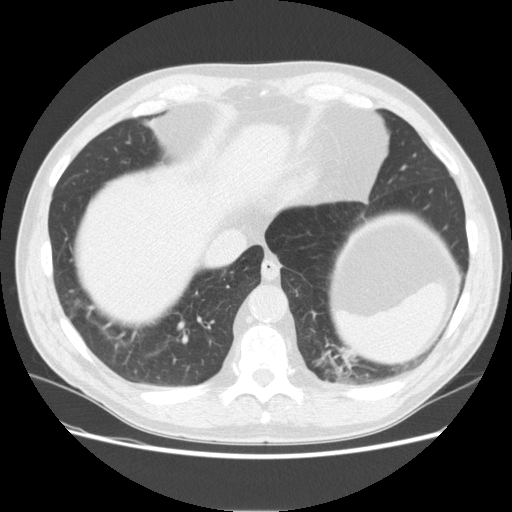
Low-dose screening chest CT, one axial slice; slice 50 of 165 in the series (ordered by position); 120 kVp; lung window (W 1500 / L -600 HU); 2.5 mm slice thickness; 512 × 512 image matrix, field of view 375 × 375 mm.
Structures marked on this image (manually delineated by an expert):
- lesion 1 (tumor, upper lobe of left lung): bounding box (x1, y1, x2, y2) in pixels: (316, 346, 366, 382)